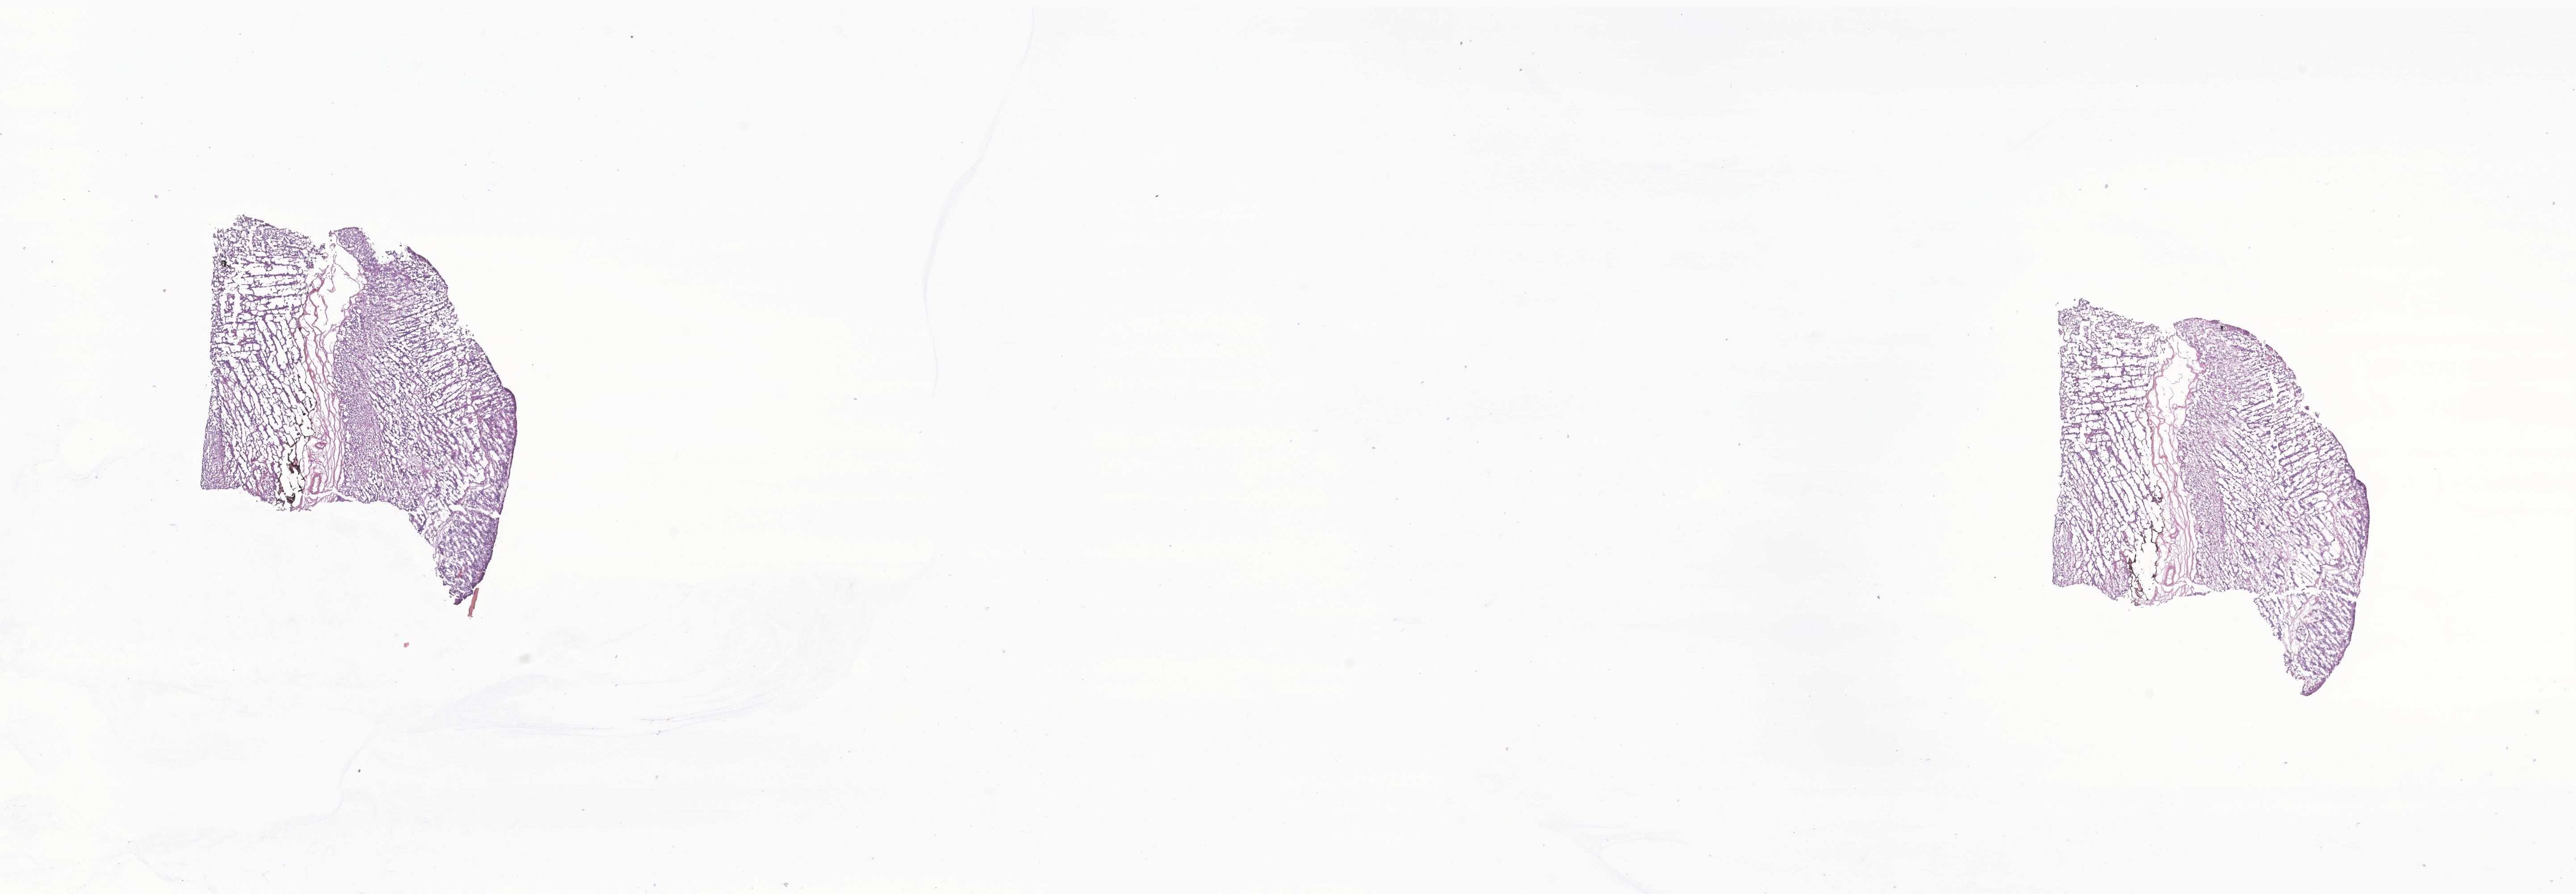
H&E whole-slide image of tumor tissue from the adrenal gland, a low-resolution overview of the entire scanned area, about 24.3 x 8.4 mm; frozen section. Patient: female, age 190 days.
Diagnosis (ICD-O-3 morphology term): Neuroblastoma, NOS.